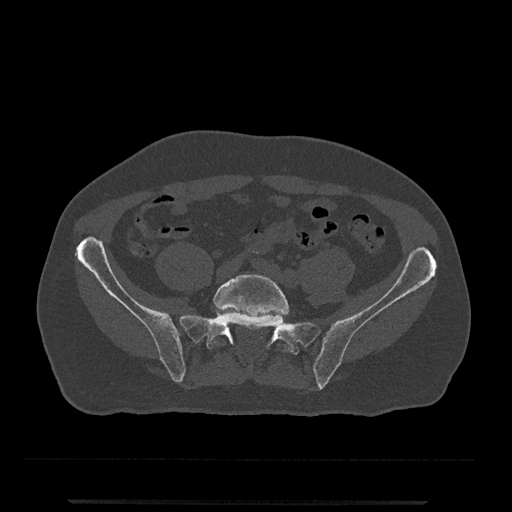
CT including the spine, one axial slice; slice 40 of 797 in the series (ordered by position); 120 kVp; bone window (W 1800 / L 400 HU); 0.5 mm slice thickness; 512 × 512 image matrix. Male patient, age 63 years. From the clinical record (not read from this slice): primary cancer: prostate.
Structures marked on this image (semi-automatic segmentation, software-assisted and operator-edited):
- L5 vertebra: box from (x=209, y=274) to (x=289, y=352) px